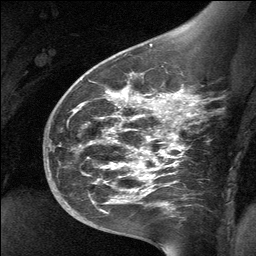
Breast MRI (dynamic contrast-enhanced), one sagittal slice. Slice 42 of 64 in the series (ordered by position). Dynamic contrast-enhanced study with each time point stored as its own series, time point 2 of 3 at this slice position (early post-contrast, ordered by acquisition time). 1.5 T. TE 4.8 ms, TR 27 ms. 256 × 256 image matrix, field of view 200 × 200 mm. Female patient, age 39 years. Case-level facts recorded for this patient, not image findings: setting: breast cancer imaged before/during neoadjuvant chemotherapy; receptor status: HER2-positive.
Annotated regions visible in this slice (semi-automatic segmentation, software-assisted and operator-edited):
- analysis volume of interest (the breast-tissue region the enhancement analysis was run in; not a lesion): box from (x=70, y=69) to (x=199, y=224) px
- tumour enhancement mask (voxels above the 90 % enhancement threshold inside the analysis volume of interest): (x=120, y=92)–(x=189, y=170)